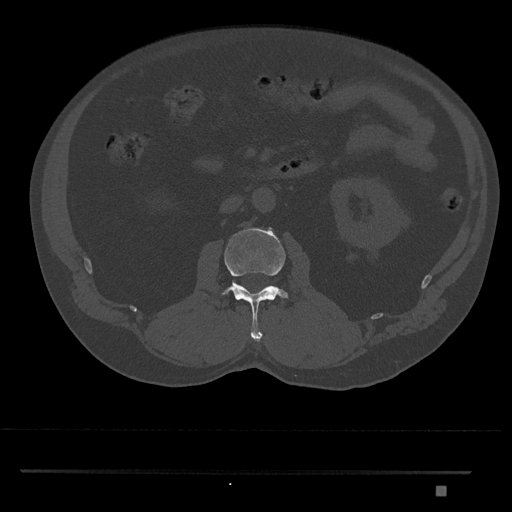
CT including the spine, one axial slice; slice 746 of 1134 in the series (ordered by position); reconstruction kernel Br40s/3; bone window (W 1800 / L 400 HU); 0.5 mm slice thickness; 512 × 512 image matrix, field of view 429 × 429 mm. Male patient, age 65 years. From the clinical record (not read from this slice): primary cancer: prostate.
Structures marked on this image (semi-automatically segmented with operator editing):
- L2 vertebra: bounding box <222,228,289,342> (left, top, right, bottom; pixels)